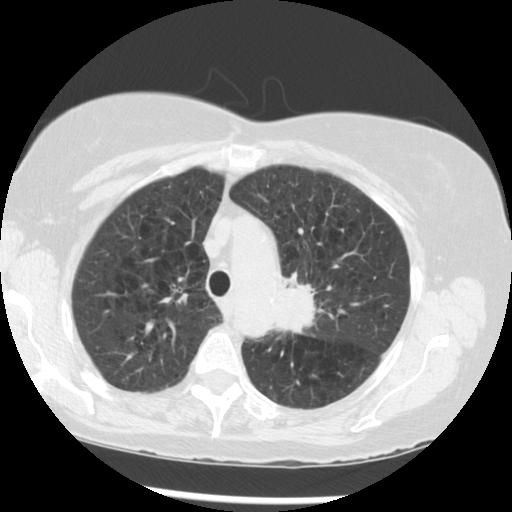
Low-dose screening chest CT, one axial slice; position 214 of 283 along the scan axis; 120 kVp; lung window (W 1500 / L -600 HU); 512 × 512 image matrix, field of view 330 × 330 mm.
Annotated regions visible in this slice (manually delineated by an expert):
- lesion 1 (tumor, upper lobe of left lung): bounding box (x1, y1, x2, y2) in pixels: (275, 274, 316, 333)